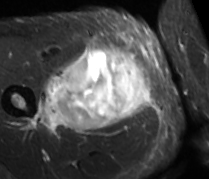
MRI of an extremity soft-tissue mass, one axial slice. Slice 36 of 89 in the series (ordered by position). STIR. MR volume resampled by the dataset authors to the PET/CT grid (not the native acquisition matrix). 3.27 mm slice thickness. 209 × 179 image matrix, field of view 204 × 175 mm. Male patient. From the clinical record (not read from this slice): histological type: undifferentiated - pleiomorphic; grade: high; site of the primary tumour: right thigh.
Outlined on this slice (expert contour drawn on MRI and transferred to this co-registered scan by the dataset authors):
- gross tumour volume including surrounding oedema: bounding box <34,44,150,131> (left, top, right, bottom; pixels)
- gross tumour volume (mass): <57,46,150,131>